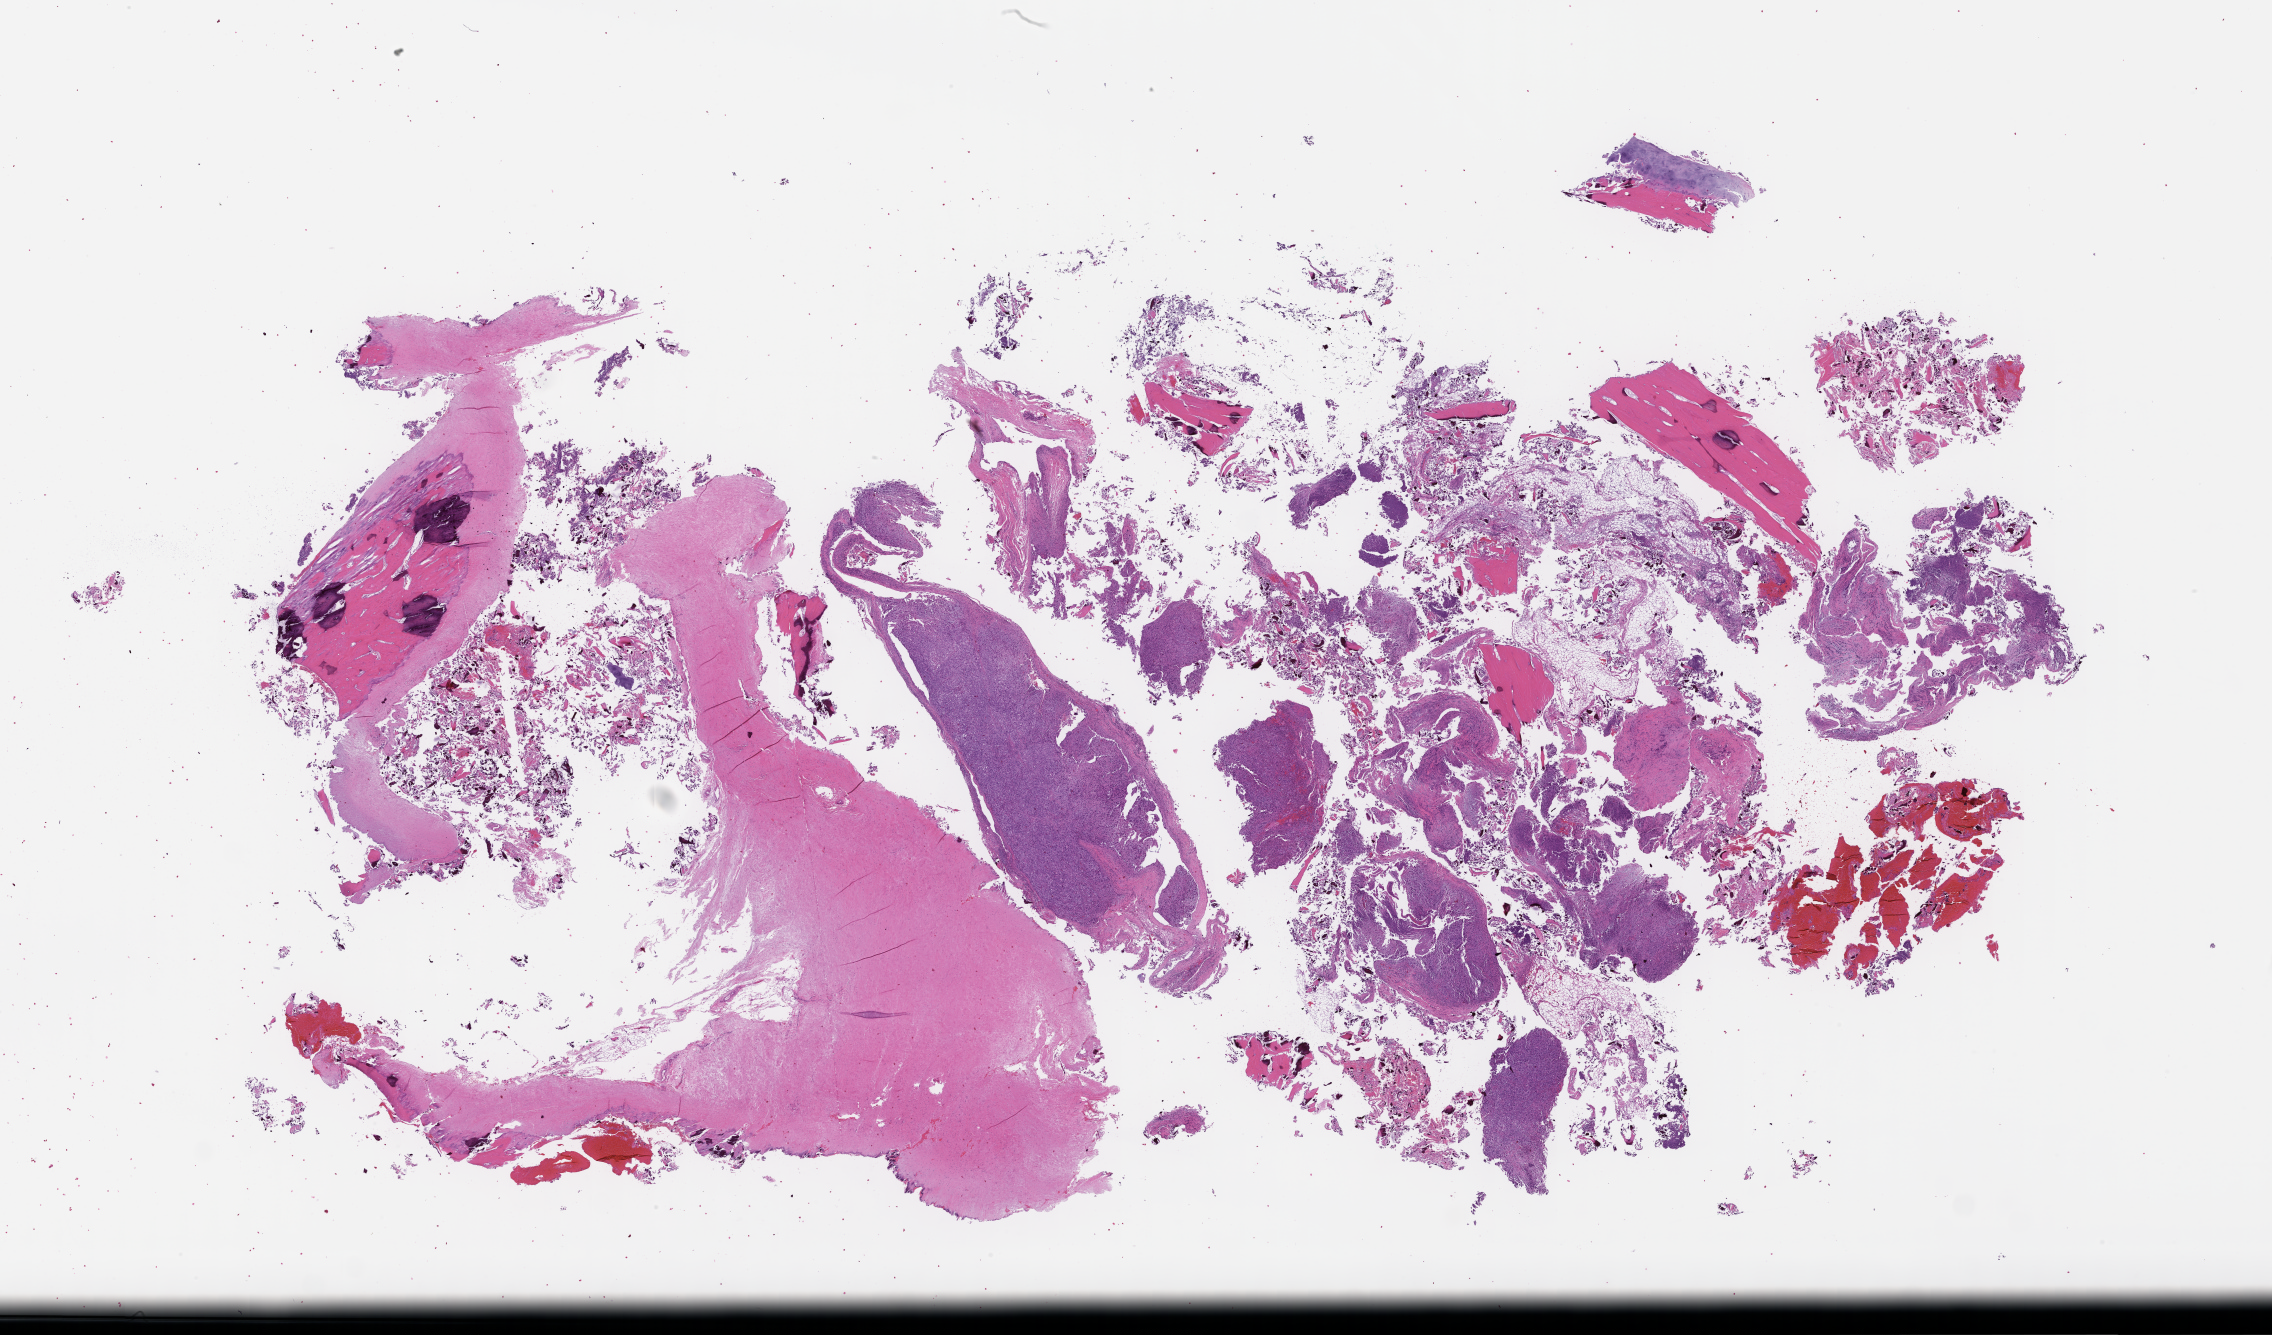
Haematoxylin and eosin whole-slide image — shown as a low-resolution overview of the whole scanned area (about 36.7 x 21.6 mm). Formalin-fixed paraffin-embedded section. Archival tissue. Patient: female.
This section: metastasis (sampled organ not recorded). Primary diagnosis of the patient: Non-Small Cell Lung Carcinoma.